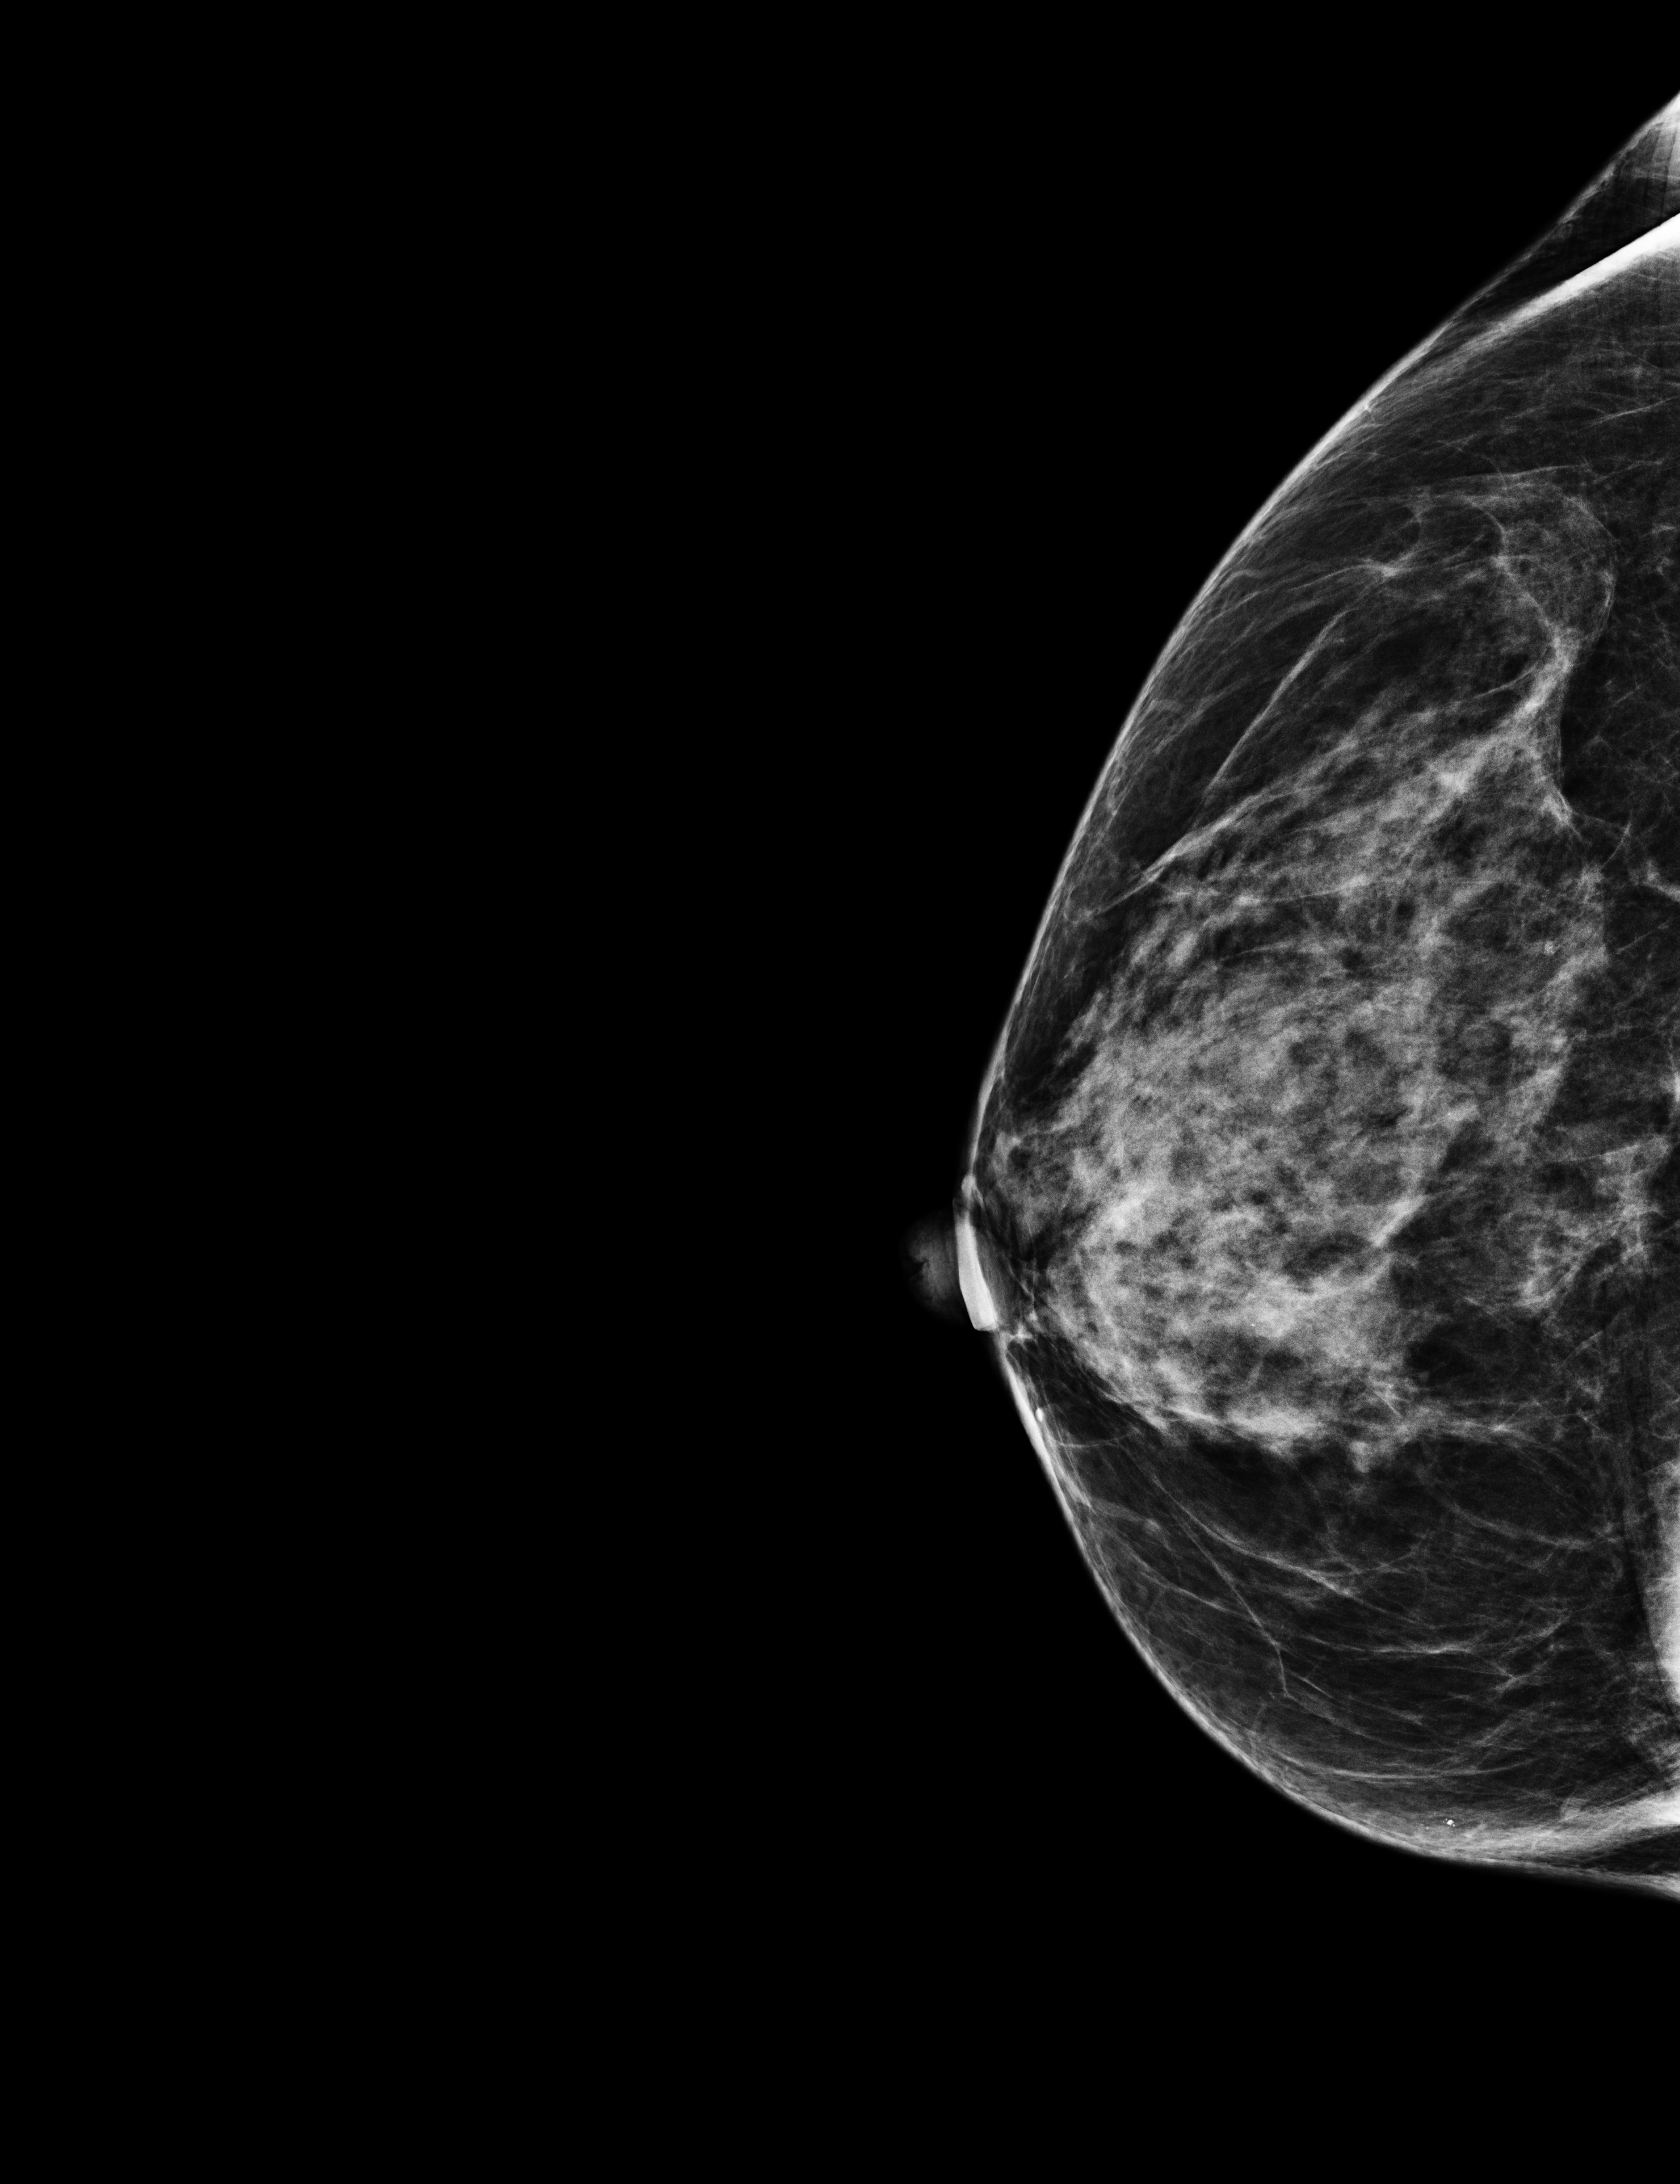
Screening examination. Patient aged 60 years (female).
Image type: full-field digital mammogram. Breast: right. Projection: craniocaudal (CC) view.